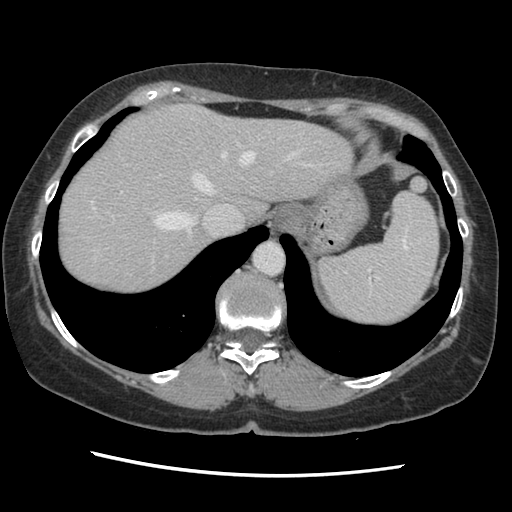
Contrast-enhanced abdominal CT, one axial slice; slice 111 of 141 in the series (ordered by position); soft-tissue window (W 400 / L 40 HU); 2.5 mm slice thickness; 512 × 512 image matrix, field of view 330 × 330 mm. Female patient, age 61 years. From the clinical record (not read from this slice): diagnosis: colorectal cancer liver metastases, imaged before liver resection; multiple liver metastases: no; largest metastasis: 2.4 cm; disease in both lobes: no.
Structures marked on this image (manually delineated by an expert):
- hepatic veins: bounding box <93,143,306,251> (left, top, right, bottom; pixels)
- liver: <58,105,352,297>
- planned liver remnant (the part of the liver to remain after resection): <58,105,352,296>